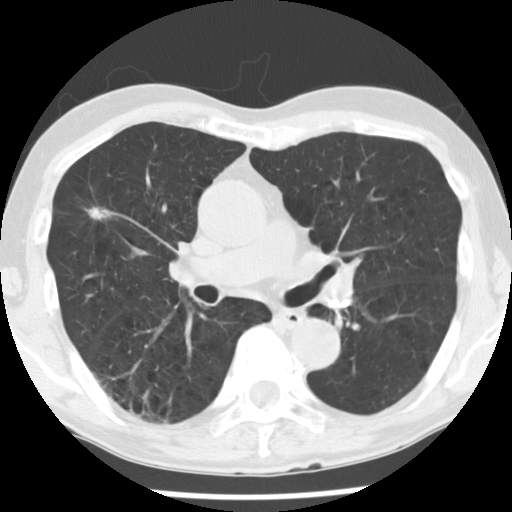
Low-dose screening chest CT, one axial slice. Slice 99 of 176 in the series (ordered by position). Lung window (W 1500 / L -600 HU). 512 × 512 image matrix, field of view 309 × 309 mm.
Structures marked on this image (expert manual segmentation):
- lesion 1 (tumor, upper lobe of right lung): bounding box [x1, y1, x2, y2] px = [87, 207, 108, 220]